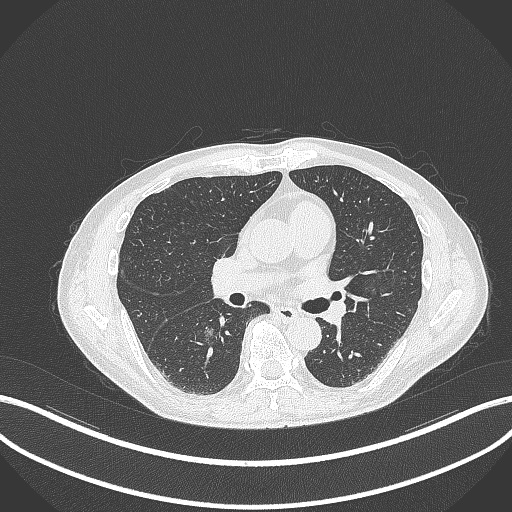
Chest CT, one axial slice; position 174 of 323 along the scan axis; lung window (W 1500 / L -600 HU); 512 × 512 image matrix. Patient: male, 61 years. From the clinical record (not read from this slice): clinical TNM (as recorded): T1c N0 M0.
Annotated regions visible in this slice (rectangle marked by the reading radiologist):
- lung tumour (recorded histology: adenocarcinoma): box from (x=202, y=324) to (x=220, y=346) px